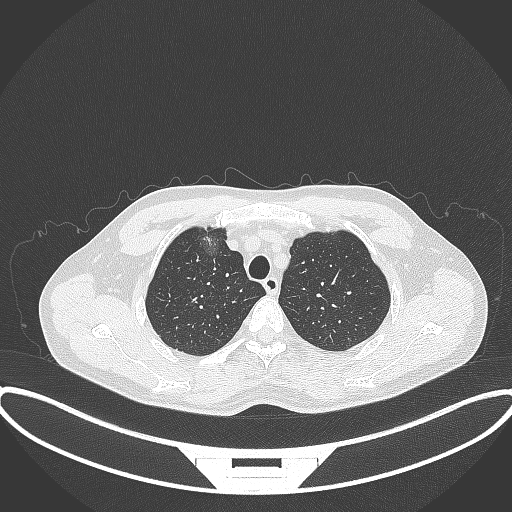
Chest CT, one axial slice; slice 300 of 395 in the series (ordered by position); lung window (W 1500 / L -600 HU); 1 mm slice thickness; 512 × 512 image matrix, field of view 424 × 424 mm. Patient: male, 60 years. Case-level facts recorded for this patient, not image findings: clinical TNM (as recorded): T1c N0 M0.
Structures marked on this image (bounding box drawn by a radiologist):
- lung tumour (recorded histology: adenocarcinoma): bounding box [x1, y1, x2, y2] px = [194, 223, 225, 259]